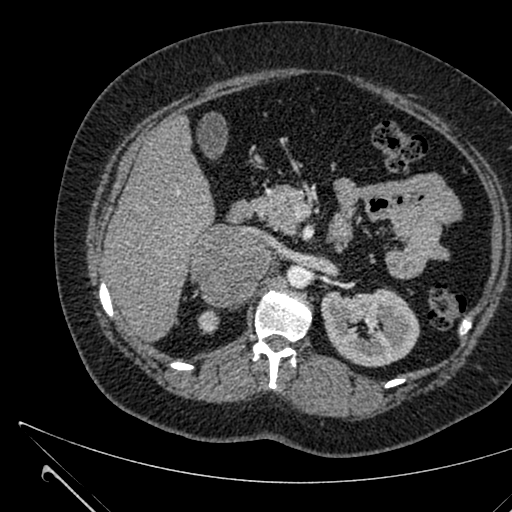
Contrast-enhanced abdominal CT, one axial slice; position 391 of 731 along the scan axis; 120 kVp; intravenous contrast given; soft-tissue window (W 400 / L 40 HU); 512 × 512 image matrix, field of view 376 × 376 mm. Patient: female, 36 years. Case-level facts recorded for this patient, not image findings: diagnosis: adrenocortical carcinoma; tumour side: right adrenal; tumour size at pathology: 10 cm; Ki-67 index: 20 %; stage (as recorded): 4.
Annotated regions visible in this slice (semi-automatically segmented with operator editing):
- mass: bounding box (x1, y1, x2, y2) in pixels: (191, 225, 266, 306)